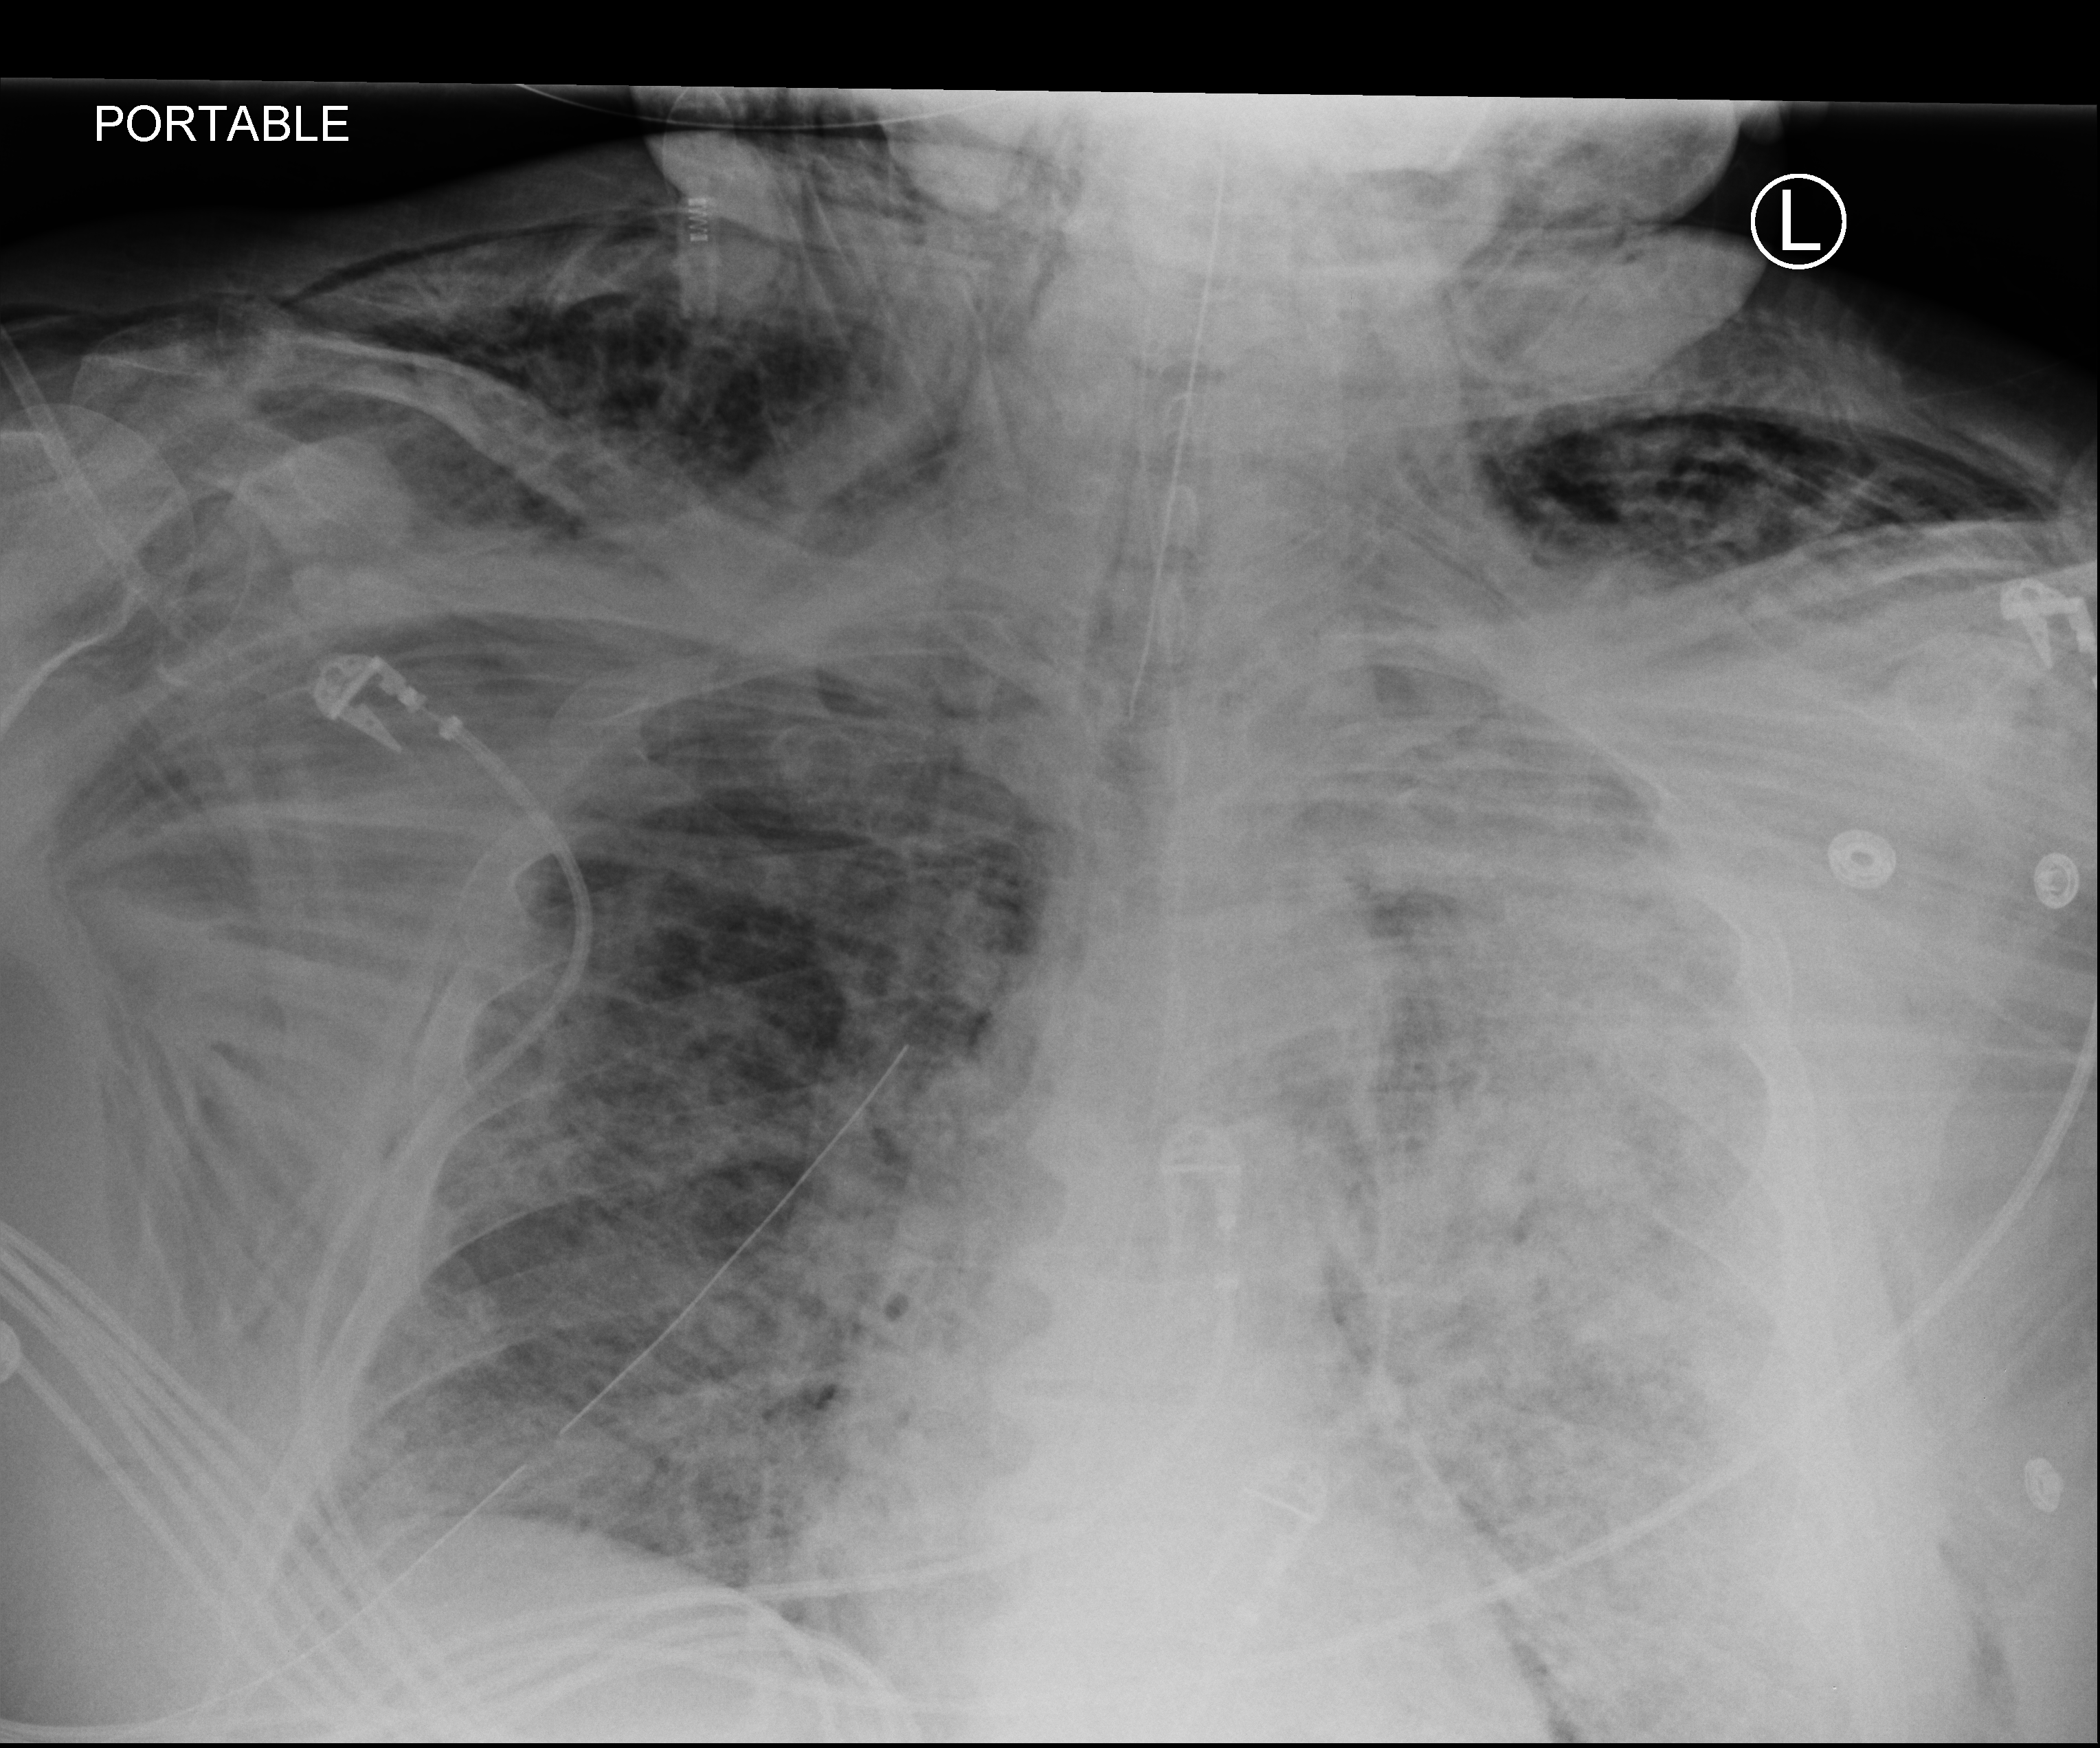
Portable chest radiograph, anteroposterior (AP) projection. Patient hospitalised with COVID-19, aged 18–59 years.
From the hospital-stay record, not from the radiograph (when in the stay this image was taken is not recorded): length of hospital stay: 28 days; admitted to intensive care during this hospital stay: yes; mechanically ventilated during this hospital stay: yes.